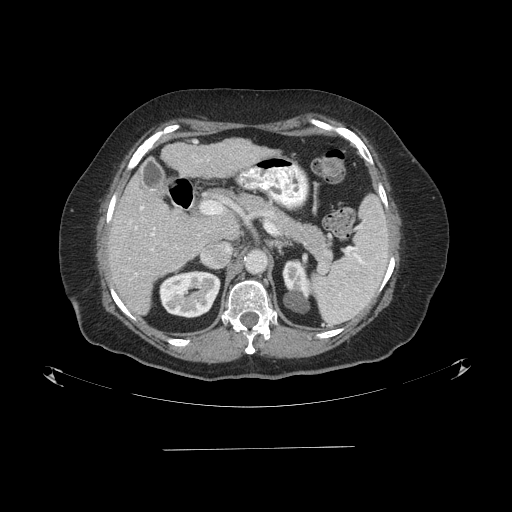
Contrast-enhanced abdominal CT (liver protocol), one axial slice. Position 47 of 103 along the scan axis. Reconstruction kernel STANDARD. One of 2 acquisitions stored at this slice position. Soft-tissue window (W 400 / L 40 HU). 2.5 mm slice thickness. 512 × 512 image matrix, field of view 500 × 500 mm. Case-level facts recorded for this patient, not image findings: diagnosis: hepatocellular carcinoma (patient treated with transarterial chemoembolisation; whether this scan precedes or follows treatment is not stated here); TNM stage (as recorded): Stage-IIIA; Child-Pugh class: A; tumour nodularity: multinodular; tumour size: 5.2 cm.
Outlined on this slice (semi-automatically segmented with operator editing):
- liver parenchyma outside the tumour (the mass and vessels are separate outlines, so this box may not span the whole liver): bounding box <106,139,272,314> (left, top, right, bottom; pixels)
- liver vessels: <130,206,154,276>